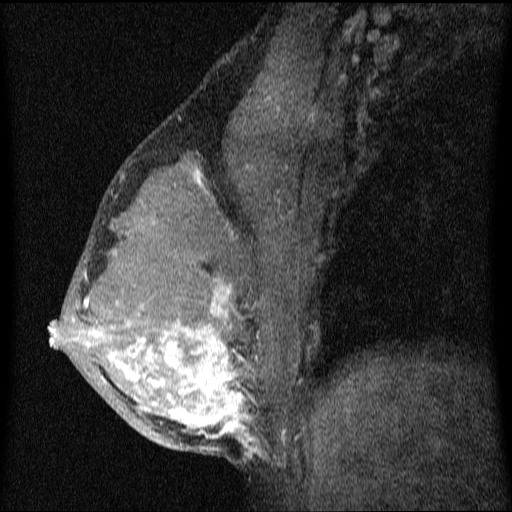
Breast MRI (dynamic contrast-enhanced), one sagittal slice; slice 40 of 64 in the series (ordered by position); dynamic contrast-enhanced series, image 2 of 4 at this slice position (ordered by acquisition); 1.5 T; TE 4.2 ms, TR 9.1 ms; 2 mm slice thickness; 512 × 512 image matrix, field of view 180 × 180 mm. Patient: female, 33 years.
Outlined on this slice (semi-automatically segmented with operator editing):
- analysis volume of interest (the breast-tissue region the enhancement analysis was run in; not a lesion): bounding box (x1, y1, x2, y2) in pixels: (50, 151, 336, 458)
- tumour enhancement mask (voxels above the 70 % enhancement threshold inside the analysis volume of interest): (50, 172, 260, 458)